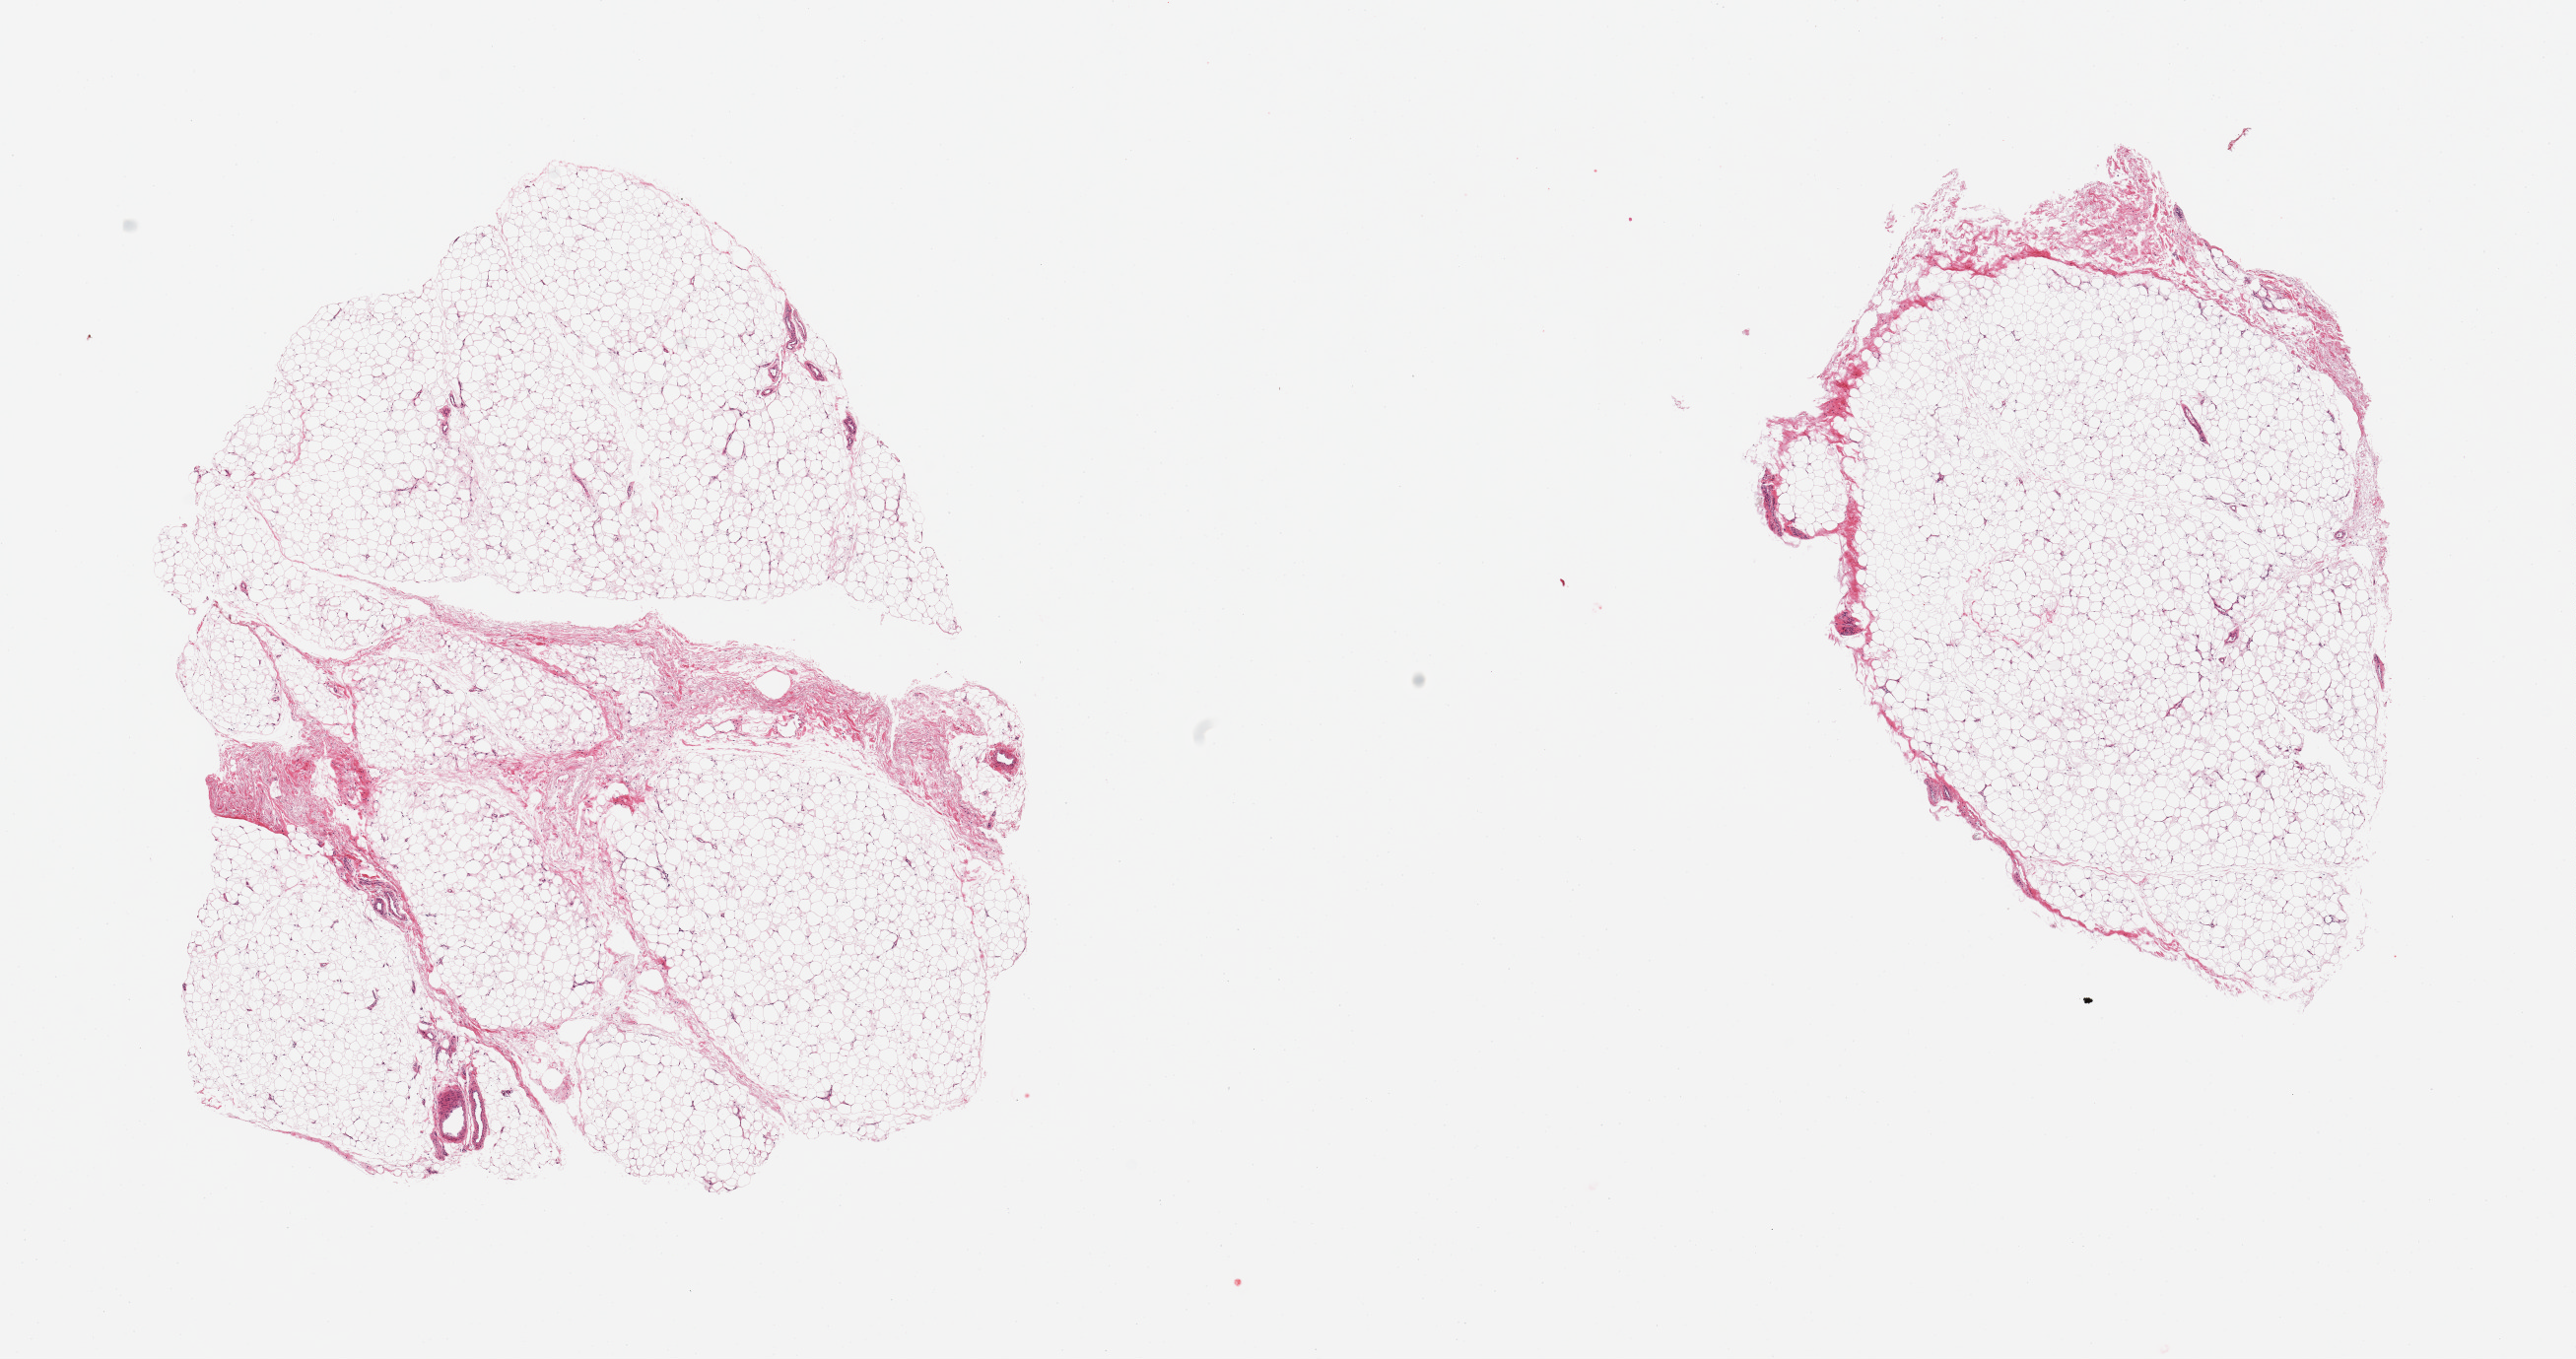
Digitized hematoxylin and eosin (H&E)-stained section, shown as a low-resolution overview of the whole scanned area (about 20.7 x 10.9 mm). PAXgene-fixed paraffin-embedded (PFPE) section. Target tissue: adipose tissue. Tissue donor sample. Male donor.
• reviewer comment on this tissue sample: 2 pieces; 5% fibrous content